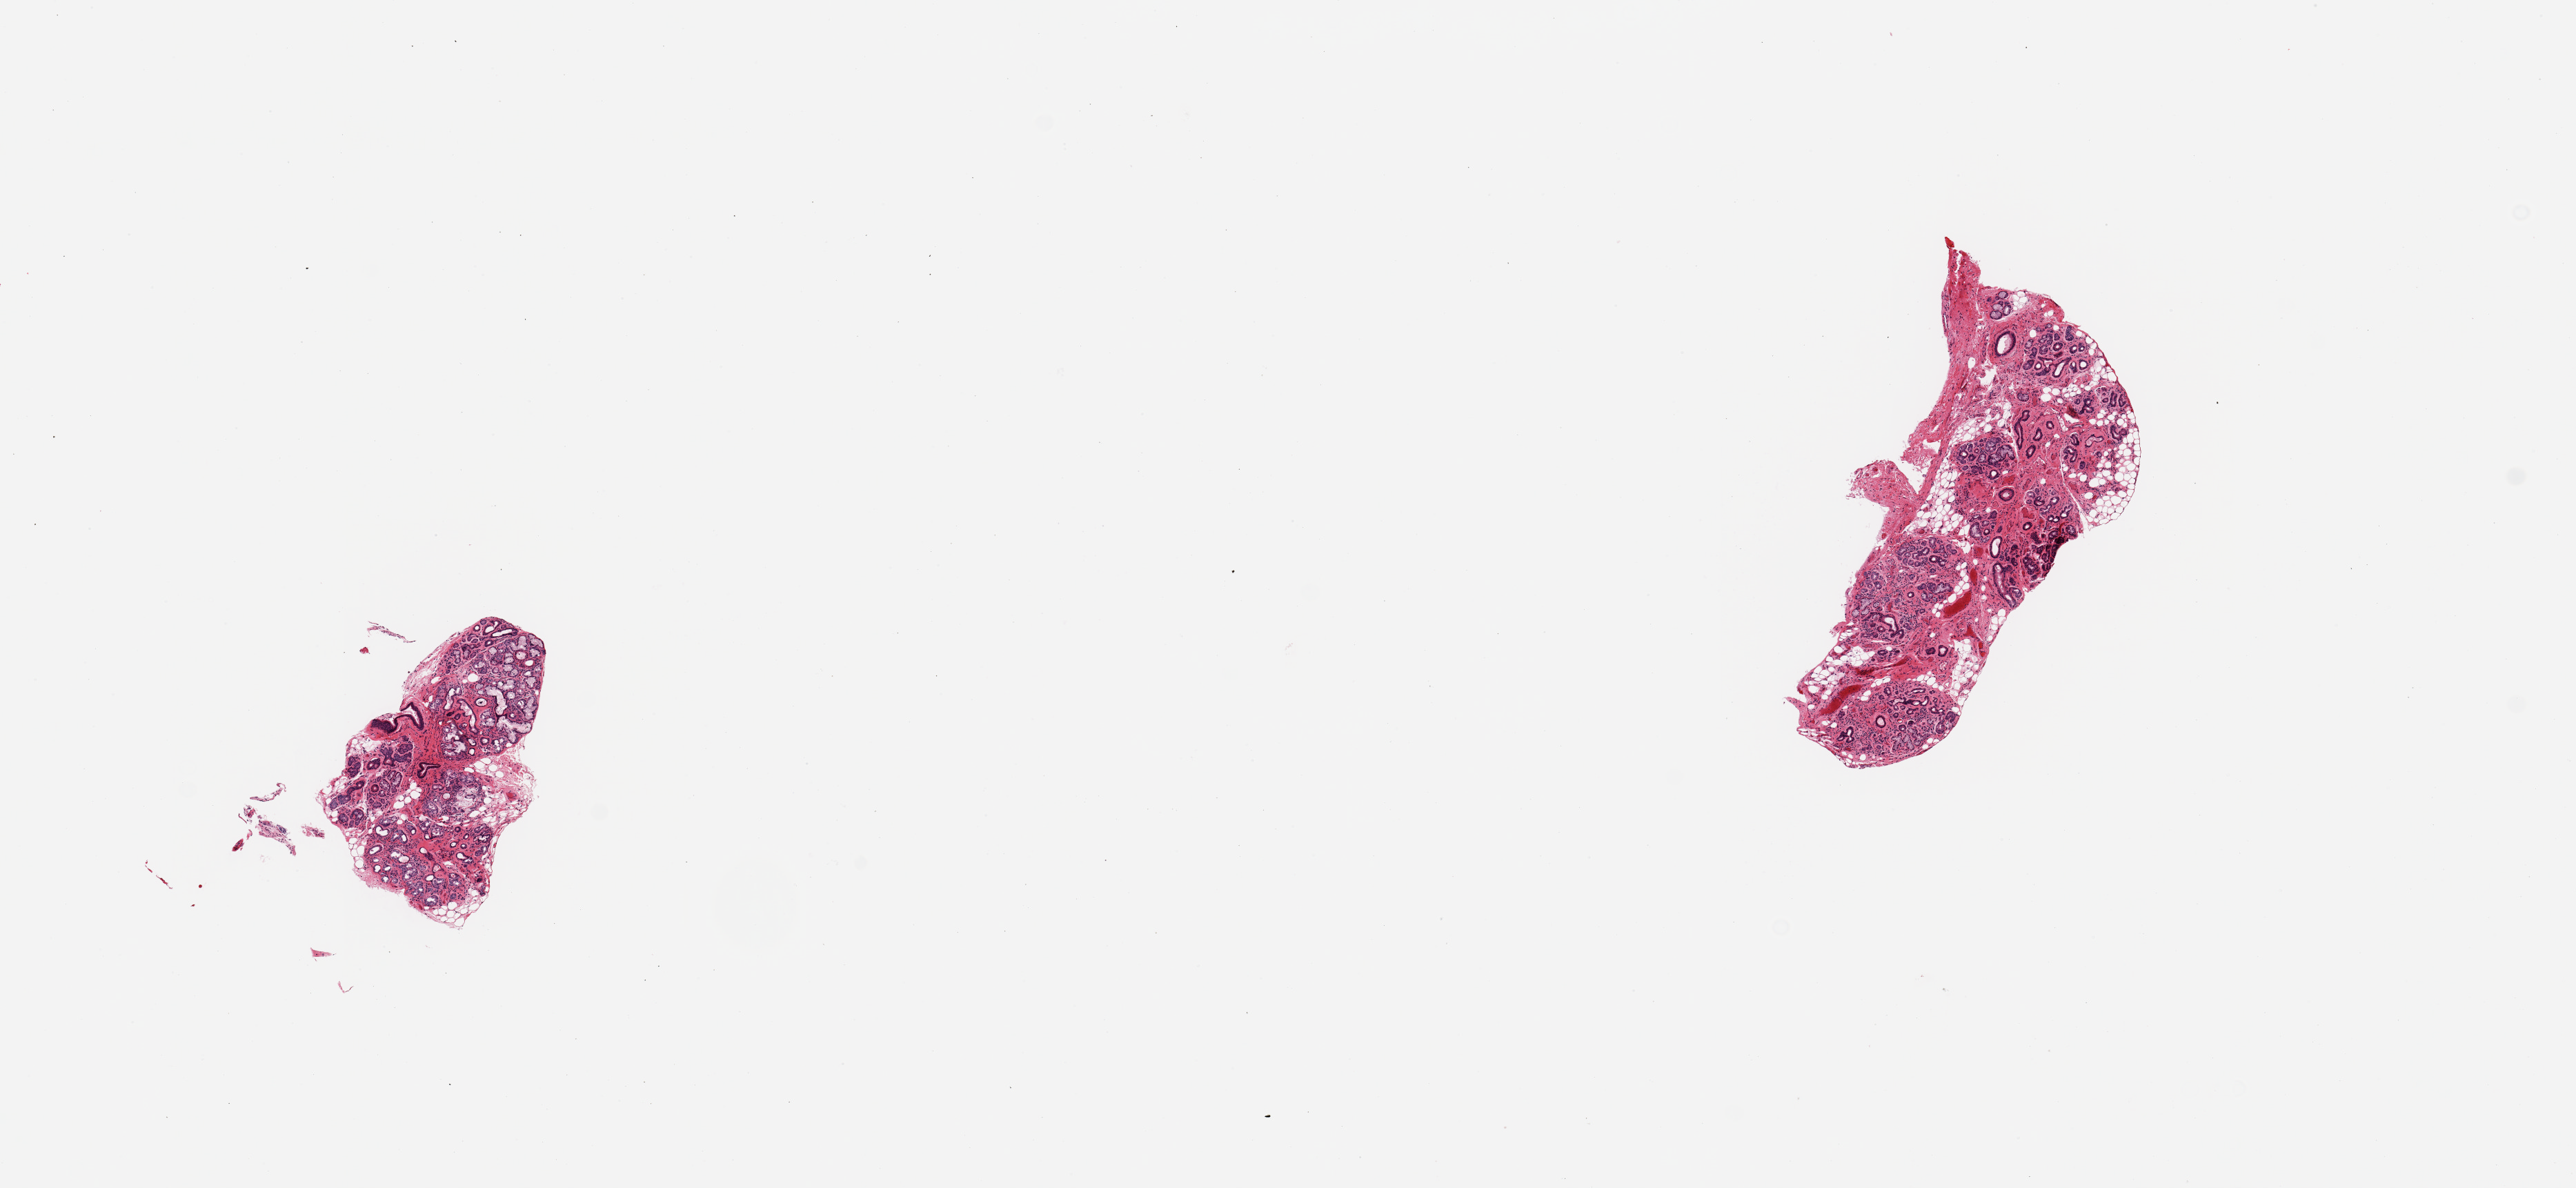
Digitized H&E-stained section, low-resolution overview of the scanned area, about 14.8 x 6.8 mm (from a 20x scan), PAXgene-fixed, paraffin-embedded tissue, section of minor salivary gland (target tissue), donor tissue sample. Donor sex: male.
• pathologist's review note for this sample: 2 pieces; well dissected, moderately atrophic glands with 20% internal fat